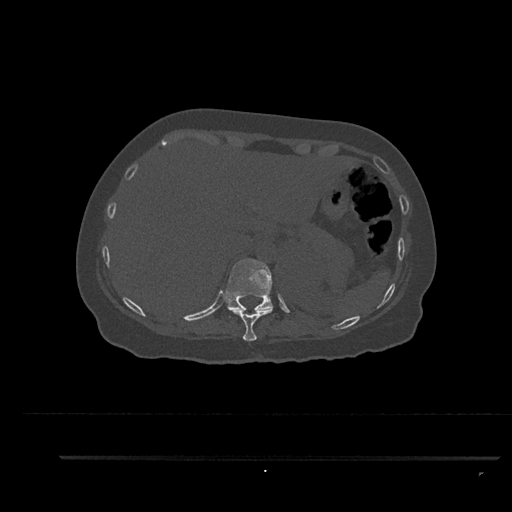
CT including the spine, one axial slice. Position 338 of 797 along the scan axis. Reconstruction kernel Br40s/3. 120 kVp. Bone window (W 1800 / L 400 HU). 0.5 mm slice thickness. 512 × 512 image matrix, field of view 408 × 408 mm. Female patient, age 44 years. From the clinical record (not read from this slice): primary cancer: renal; vertebrae with lytic lesions (as recorded): L1.
Outlined on this slice (semi-automatically segmented with operator editing):
- T10 vertebra: box from (x=227, y=308) to (x=273, y=341) px
- T11 vertebra: (x=226, y=259)–(x=273, y=318)